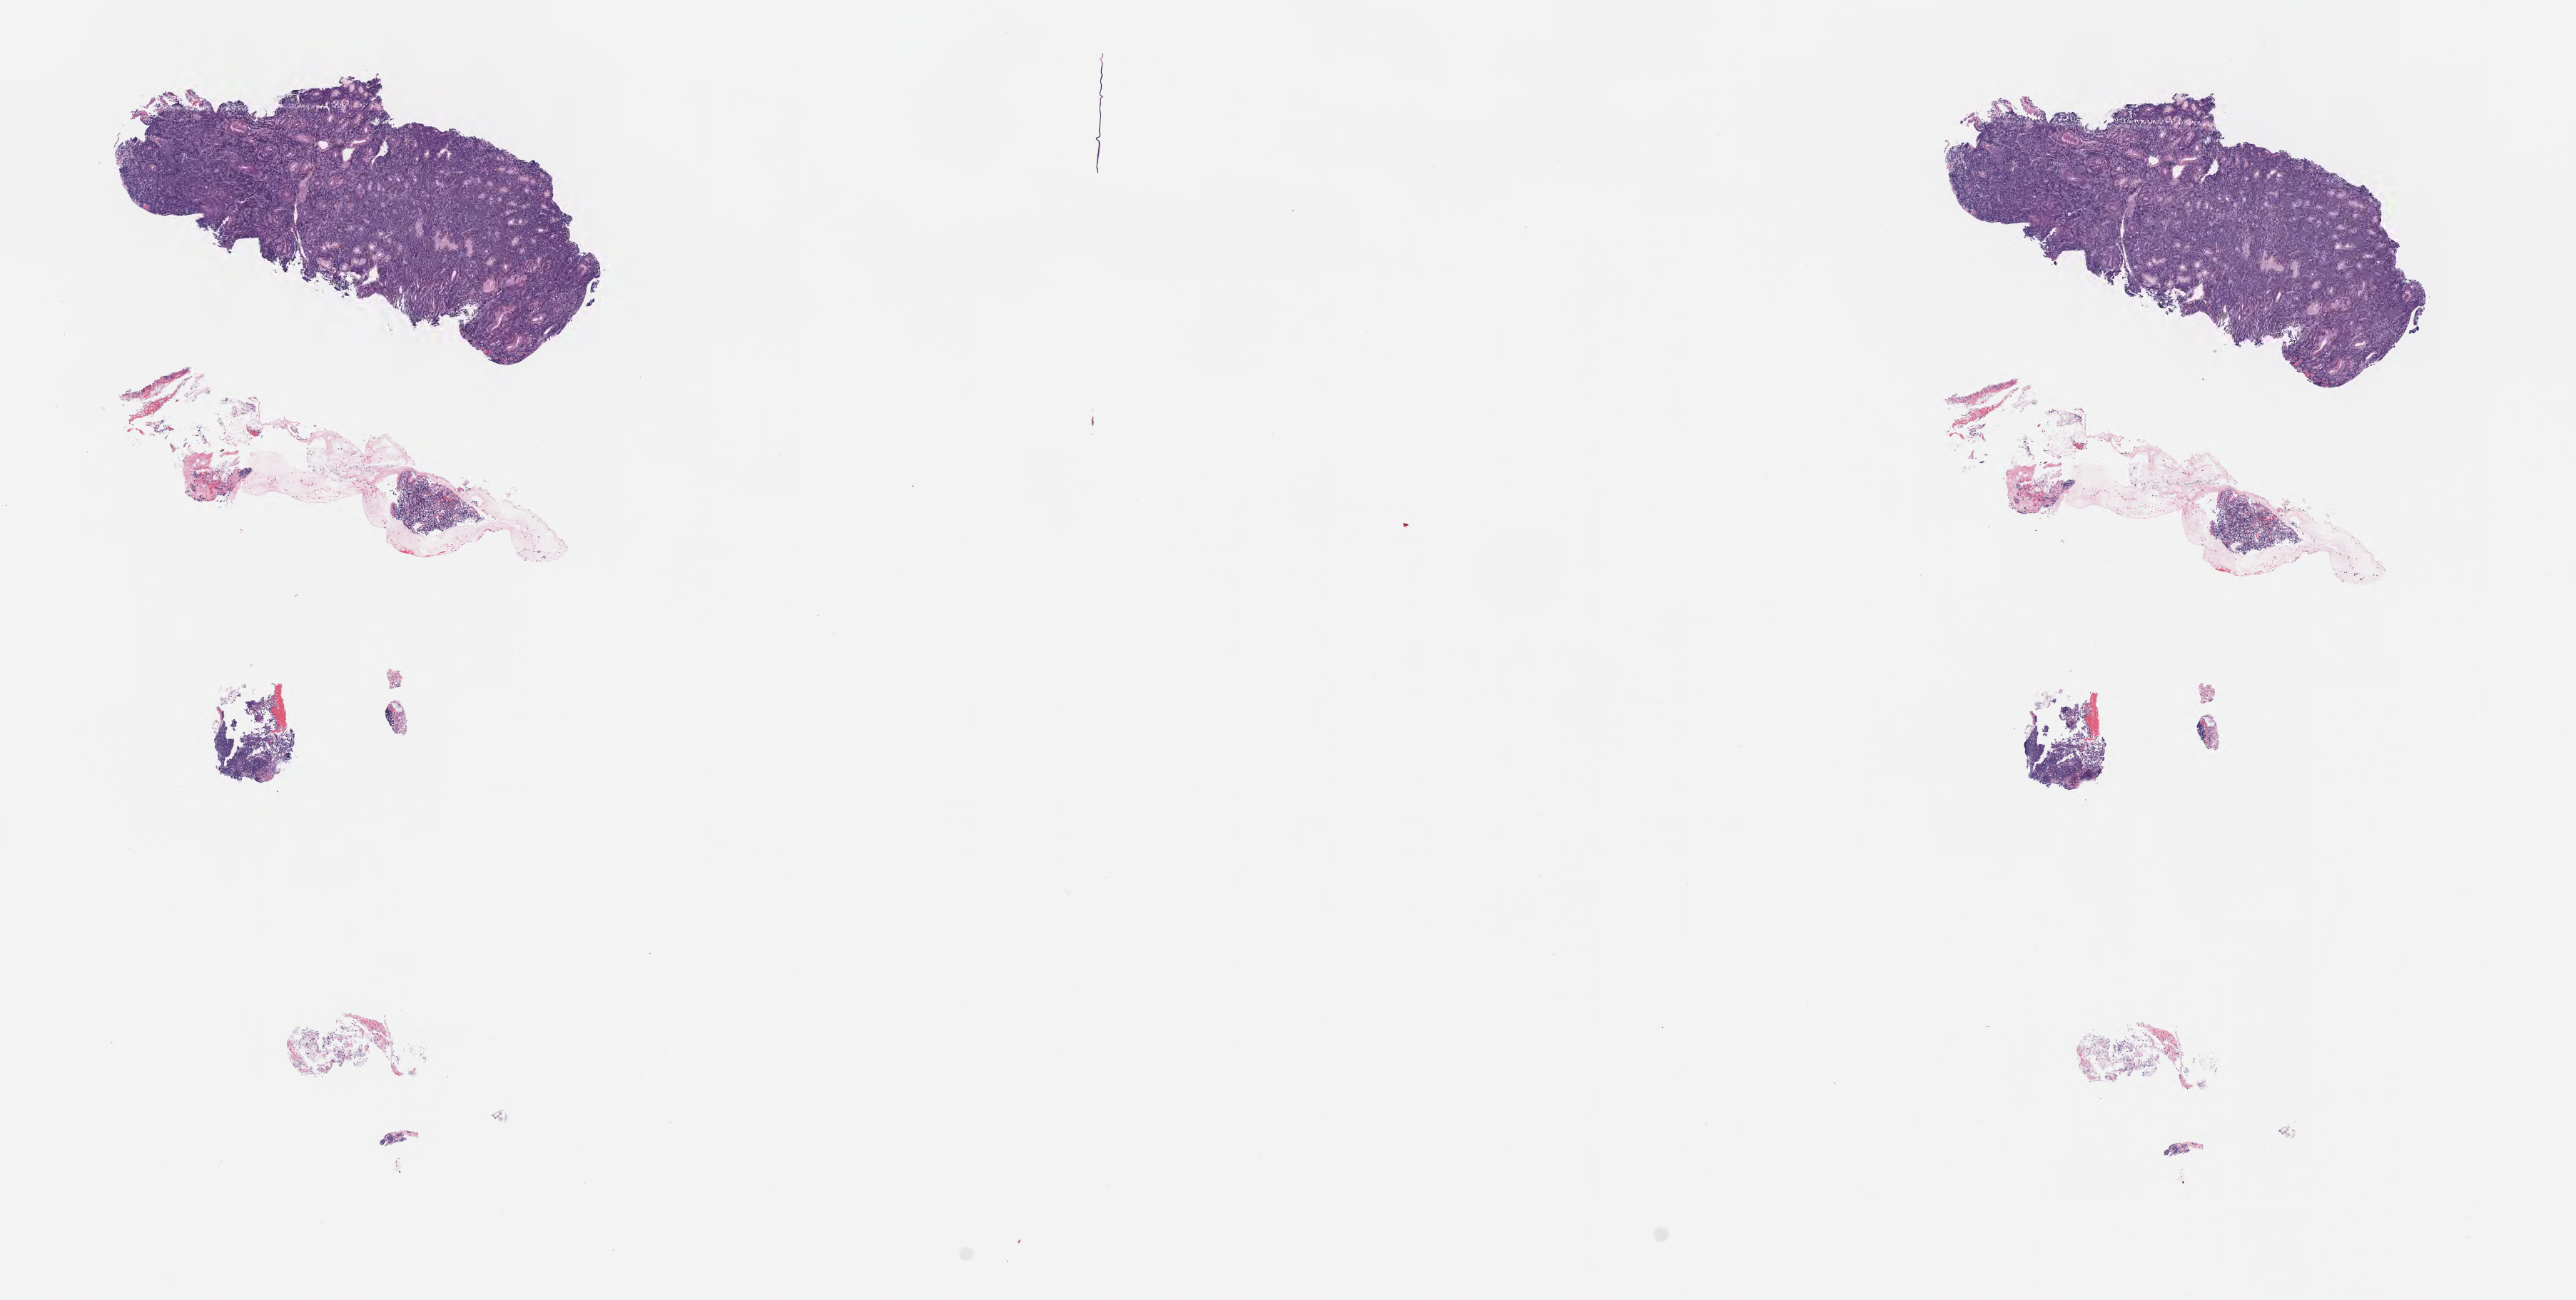
Hematoxylin and eosin (H&E) whole-slide image — whole scanned area (about 14.6 x 7.4 mm) shown as a low-resolution overview, specimen: tumor tissue, site: stomach. Patient: female, 28 years old.
Histologic diagnosis: Burkitt lymphoma, NOS.